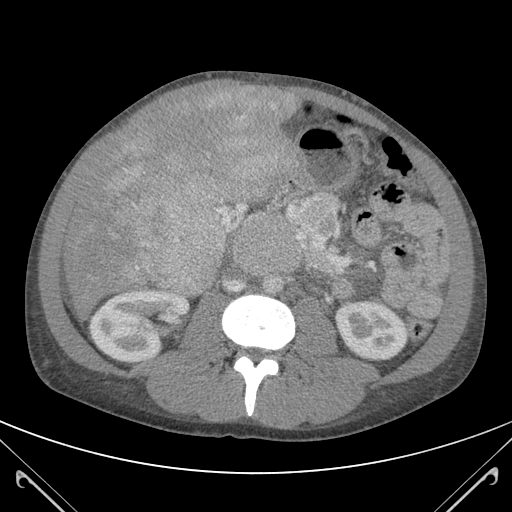
Contrast-enhanced abdominal CT (liver protocol), one axial slice; slice 46 of 118 in the series (ordered by position); soft-tissue window (W 400 / L 40 HU); 512 × 512 image matrix. Case-level facts recorded for this patient, not image findings: diagnosis: hepatocellular carcinoma (patient treated with transarterial chemoembolisation; whether this scan precedes or follows treatment is not stated here); TNM stage (as recorded): Stage-IIIB; Child-Pugh class: A; tumour nodularity: uninodular.
Annotated regions visible in this slice (semi-automatically segmented with operator editing):
- abdominal aorta: bounding box [x1, y1, x2, y2] px = [264, 275, 283, 296]
- liver parenchyma outside the tumour (the mass and vessels are separate outlines, so this box may not span the whole liver): [63, 86, 291, 313]
- mass: [96, 86, 297, 293]
- liver vessels: [217, 231, 223, 249]